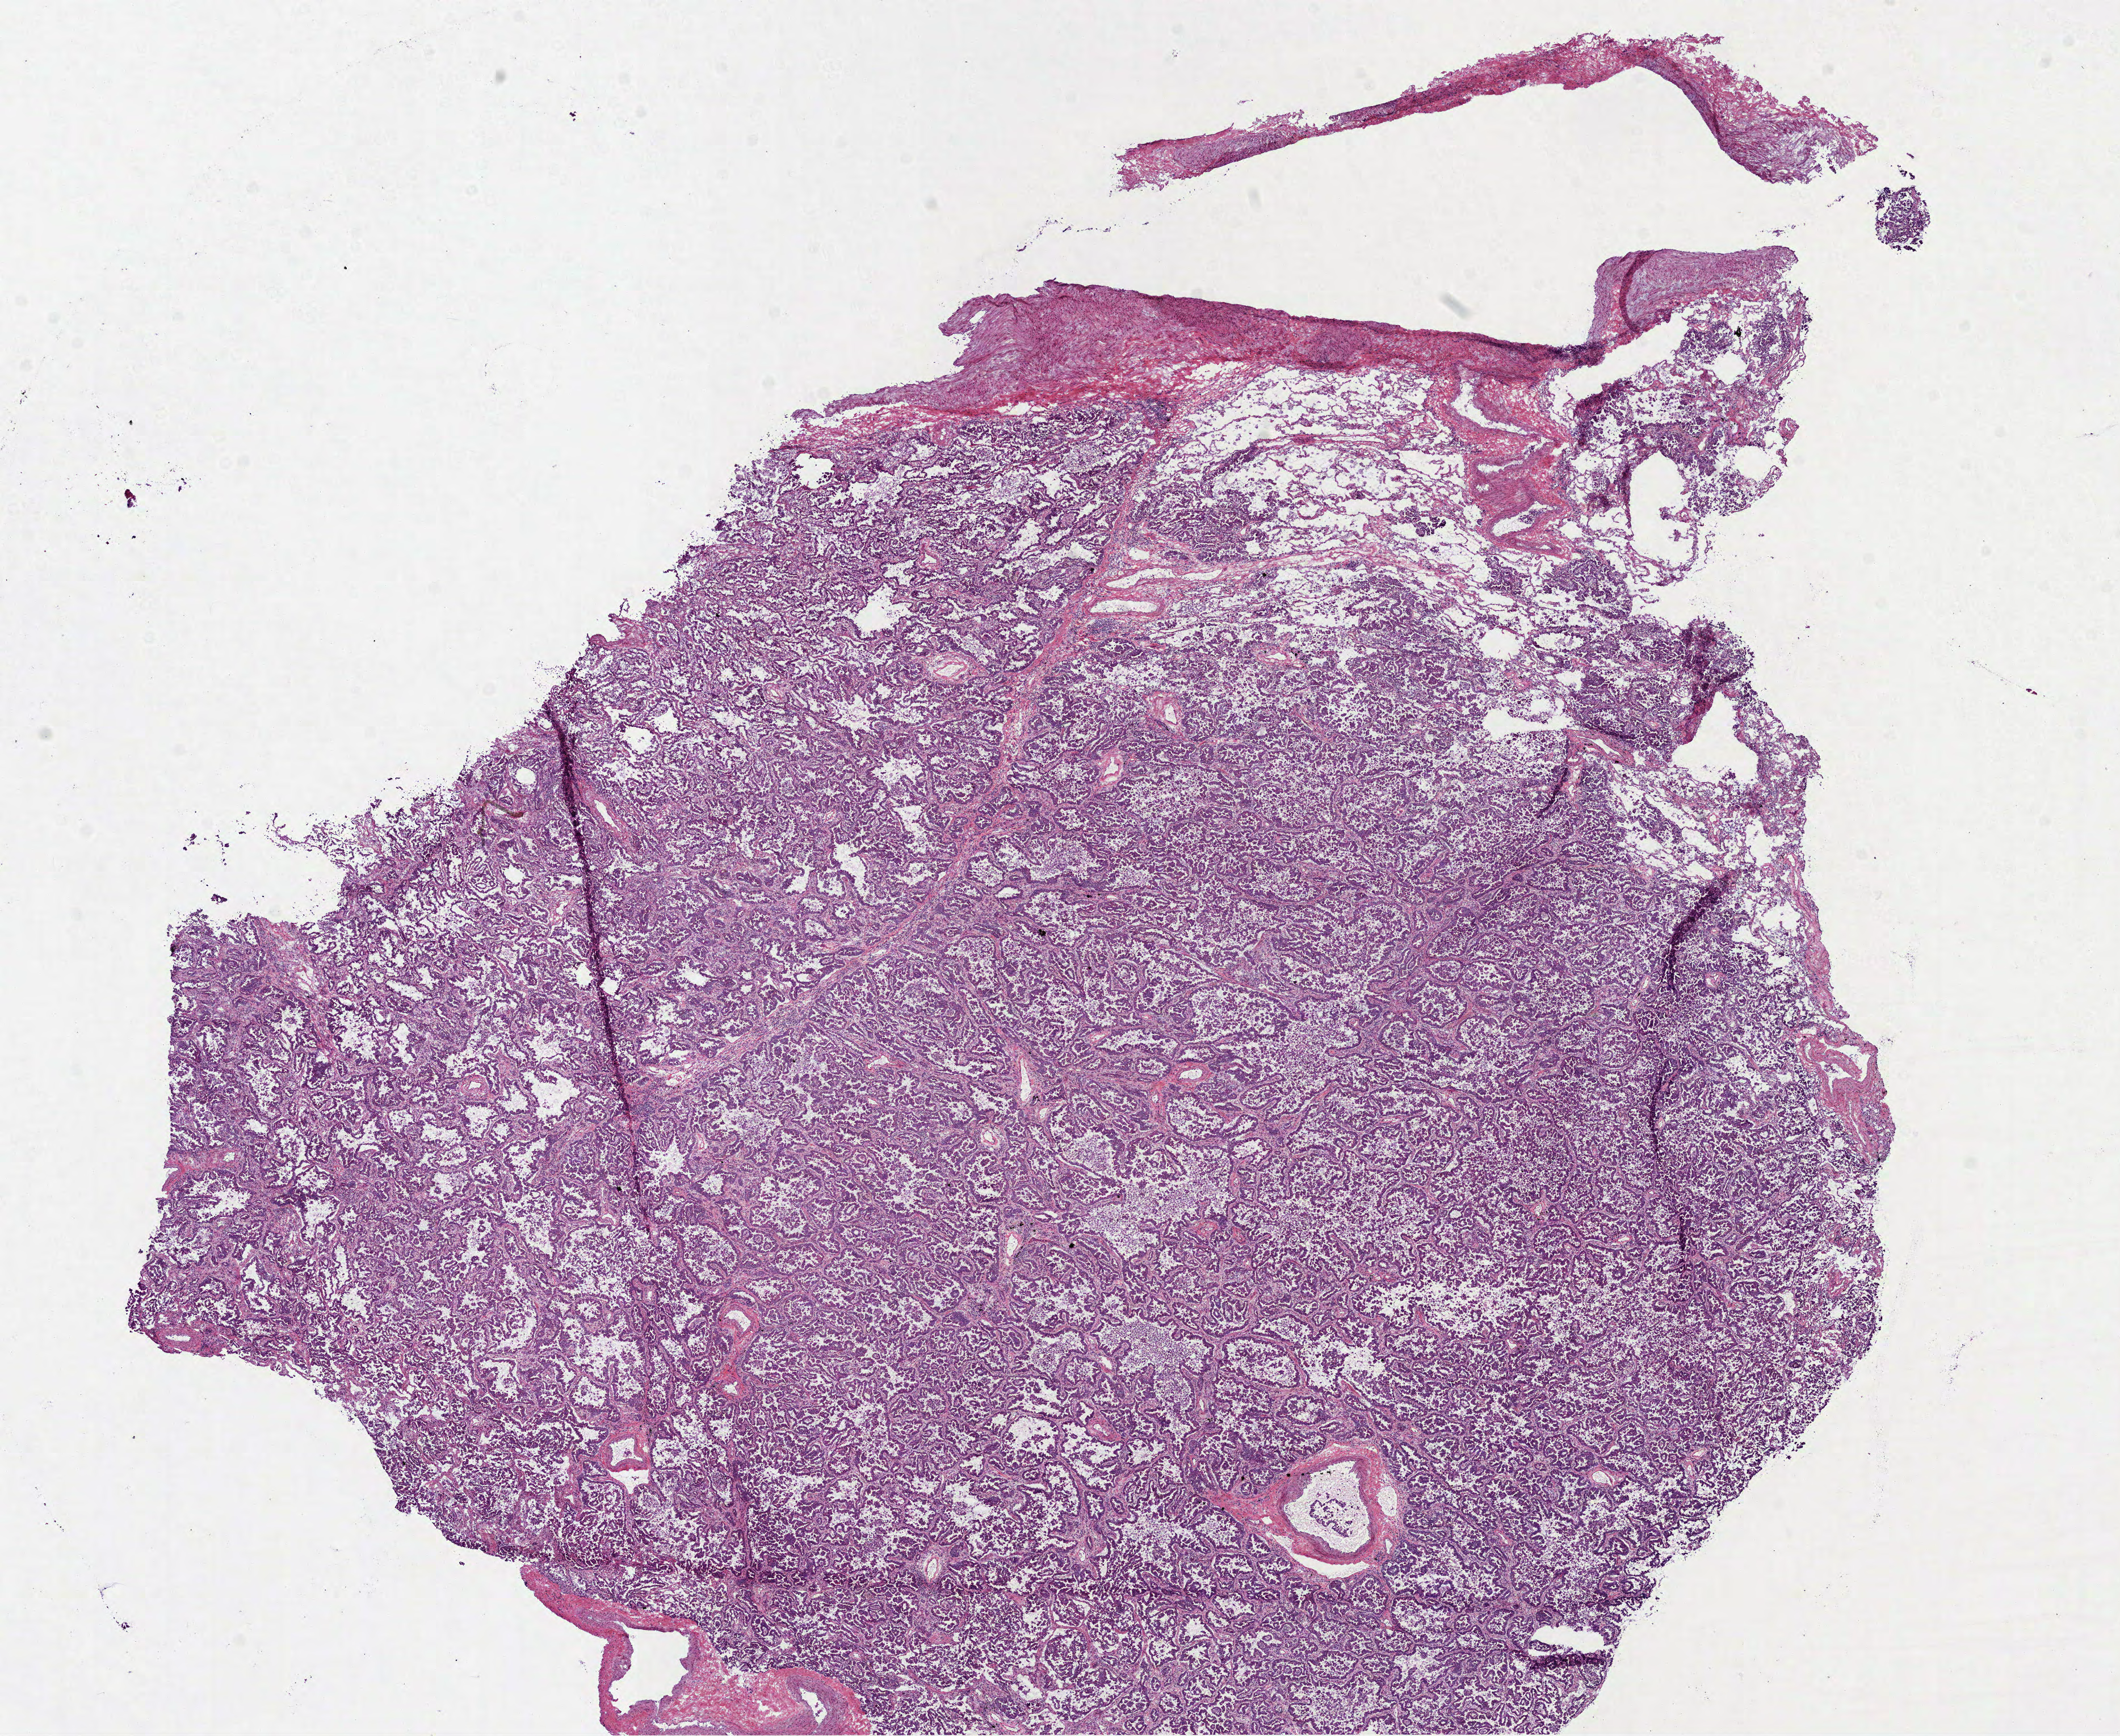
Digitized H&E-stained tissue section (whole slide) — low-resolution overview of the scanned area, about 15.1 x 12.3 mm (from a 40x scan). Frozen section from the top of the tissue portion. Lung, primary tumour sample. Male, age 75 years at initial diagnosis. Pathologist review of this section (percent, as recorded): tumour cells 95%, tumour nuclei 80%, normal cells 0%, stromal cells 5%, necrosis 0%. Inflammatory infiltration, as recorded: lymphocyte infiltration 10%, monocyte infiltration 5%, neutrophil infiltration 0%.
• AJCC pathologic stage: IIB (5th edition)
• histologic diagnosis: Adenocarcinoma, NOS (upper lobe, lung)